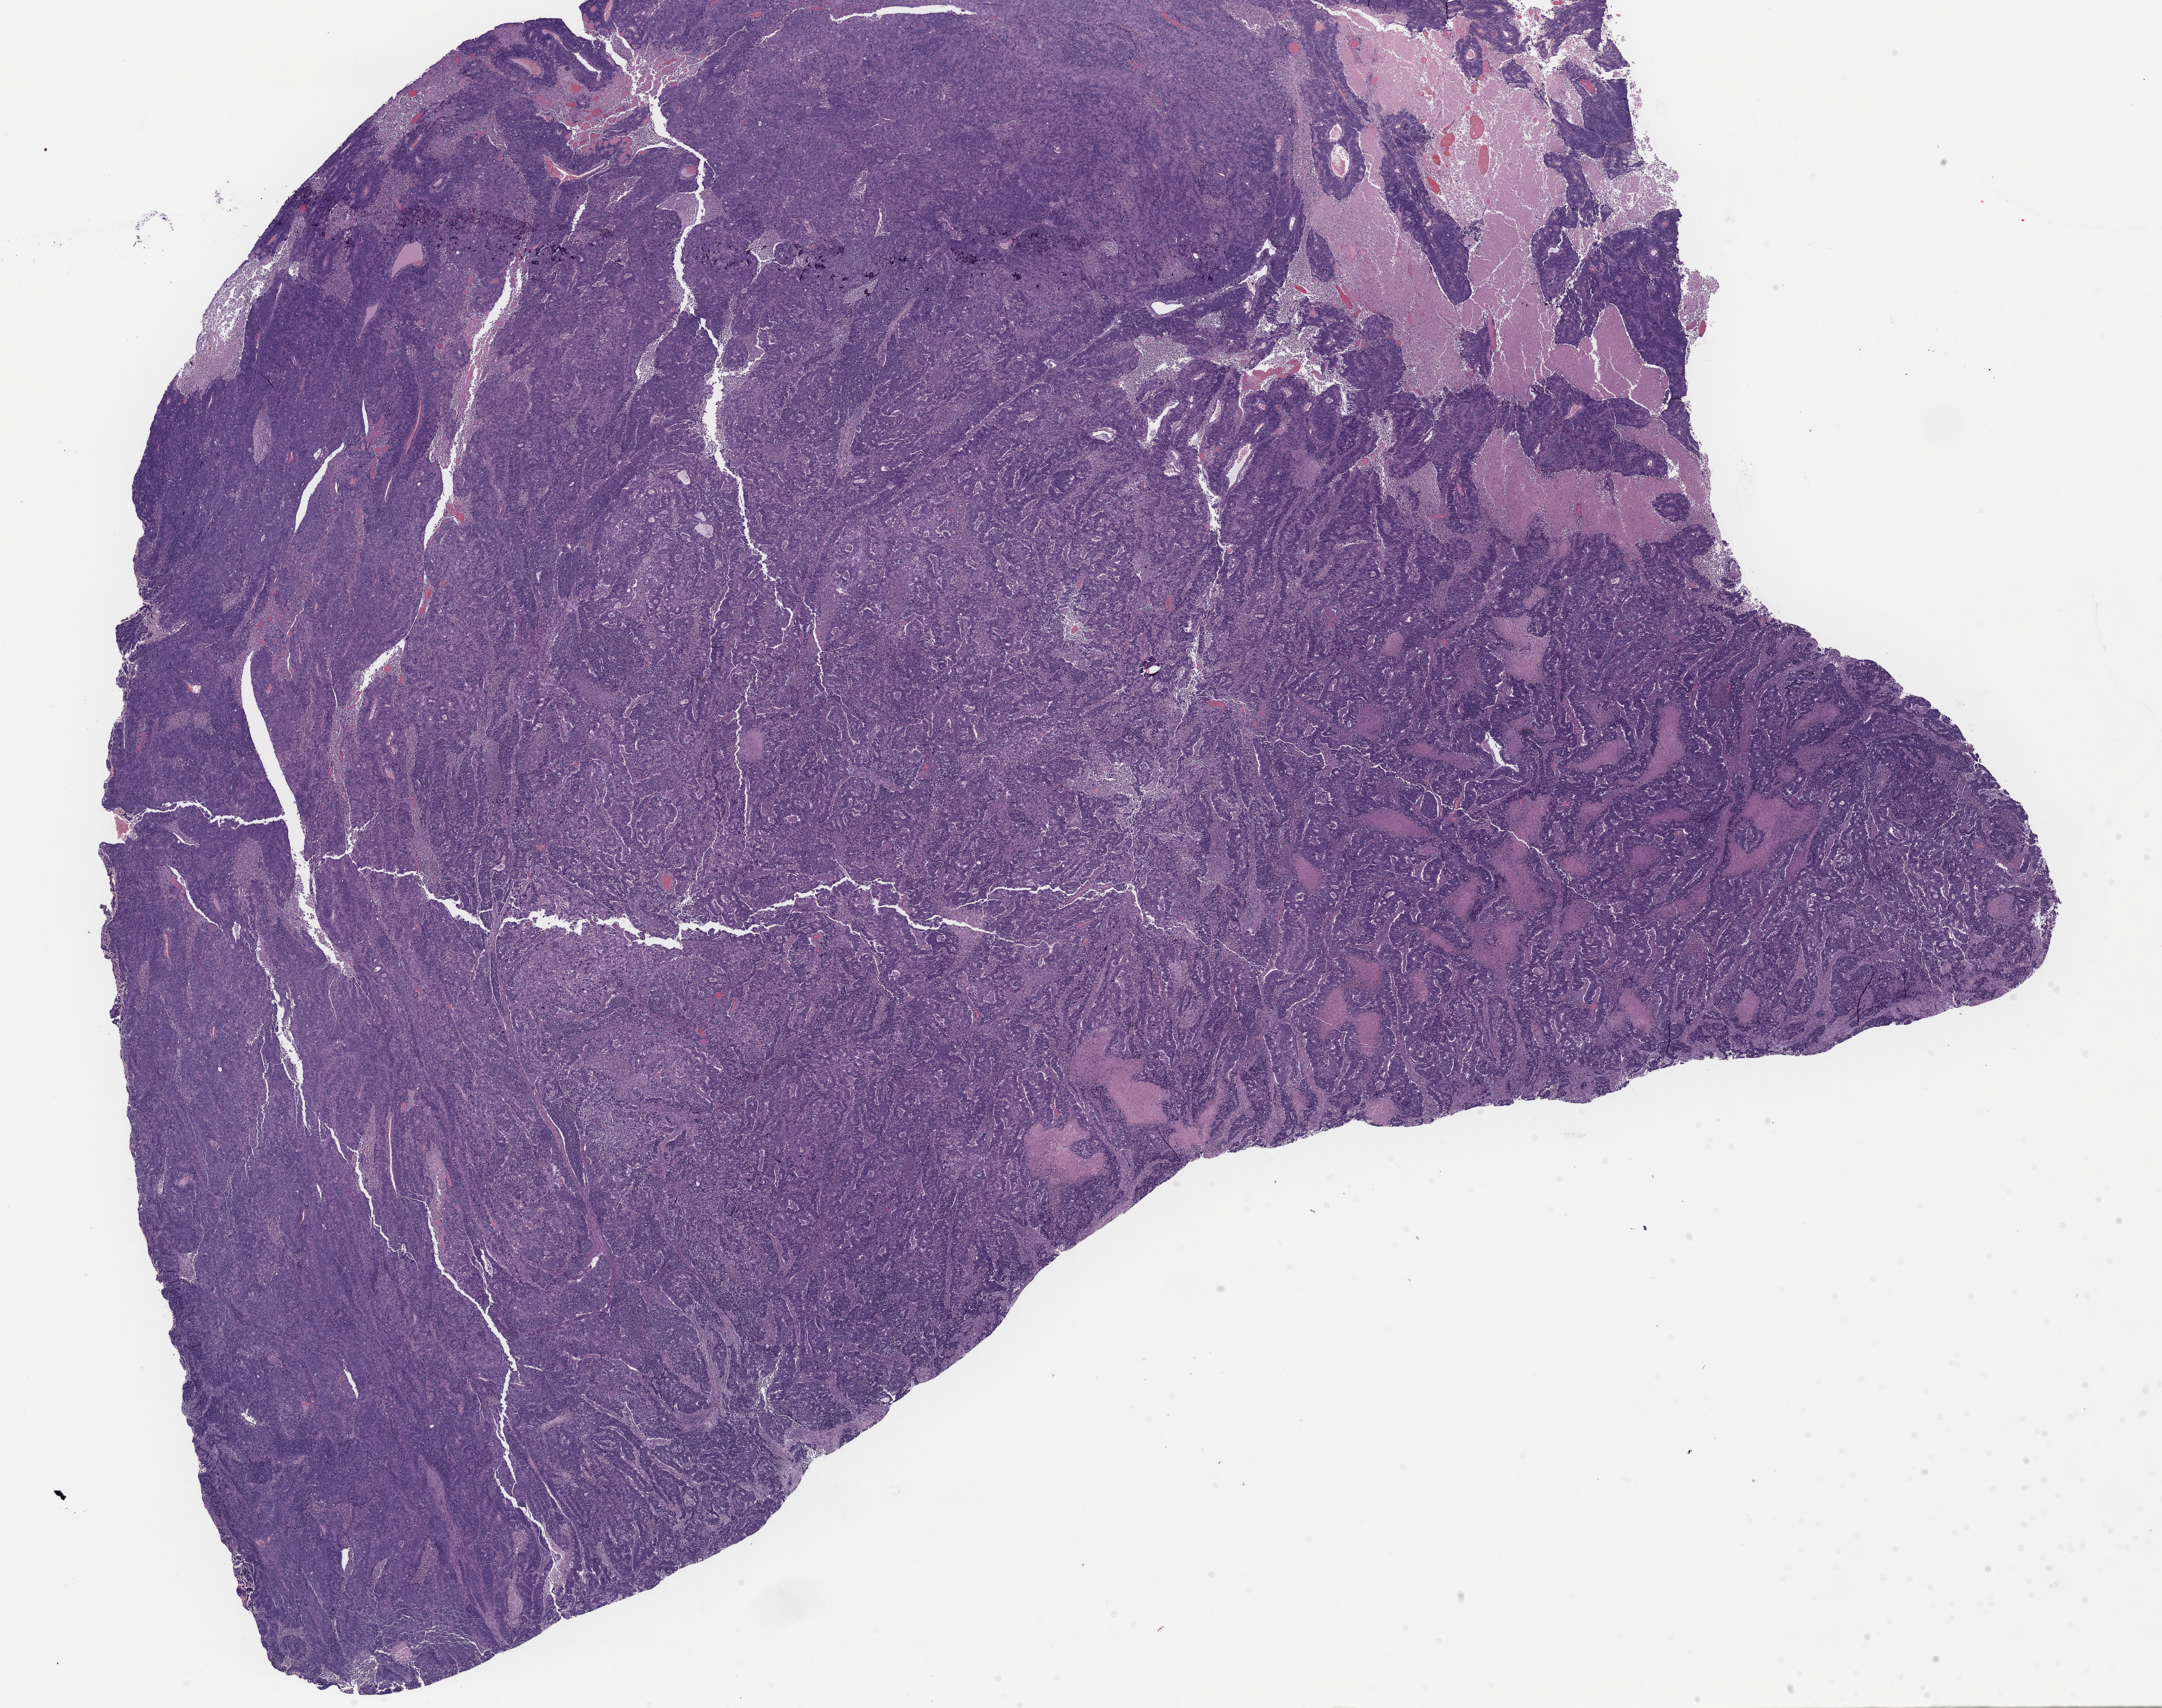
H&E-stained whole-slide image, shown as a low-resolution overview of the whole scanned area (about 26.3 x 20.8 mm, acquisition: 40x scan). FFPE section. Sample: primary tumour, uterus. Patient: female, age at initial diagnosis 82 years. Histologic grade: G3 (poorly differentiated).
- FIGO stage: II
- pathologic diagnosis: Serous cystadenocarcinoma, NOS (endometrium)